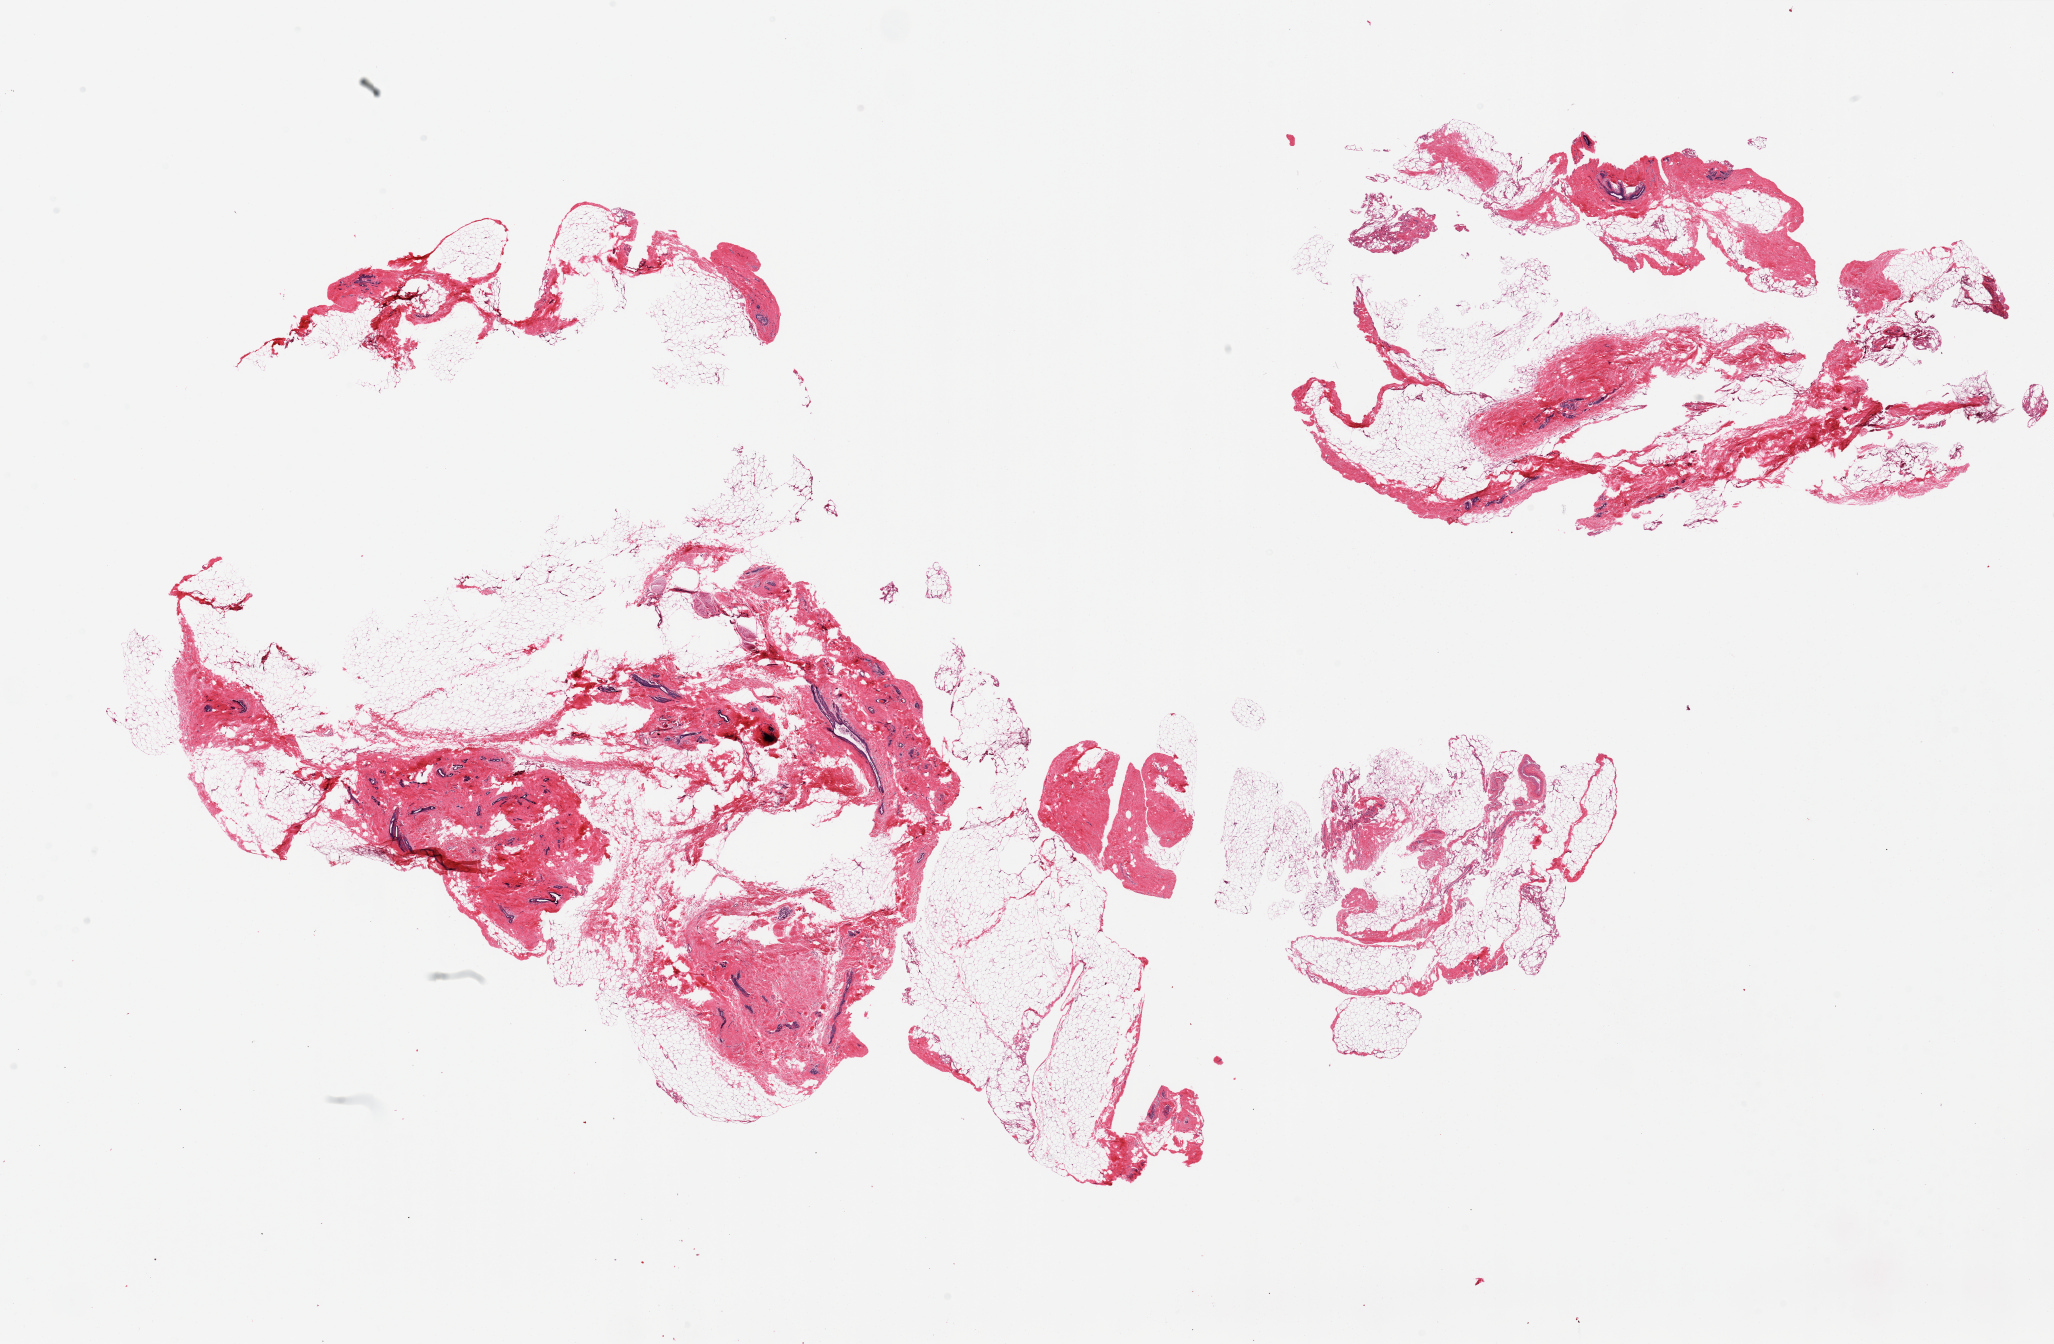
Digitized haematoxylin and eosin-stained section — whole scanned area (about 32.5 x 21.3 mm) shown as a low-resolution overview, PAXgene-fixed, paraffin-embedded tissue, sampled site (target tissue): breast, donor tissue sample. Donor sex: female.
Pathologist's review note for this sample: 2 pieces; atrophic ducts and lobular units; abundant fat.